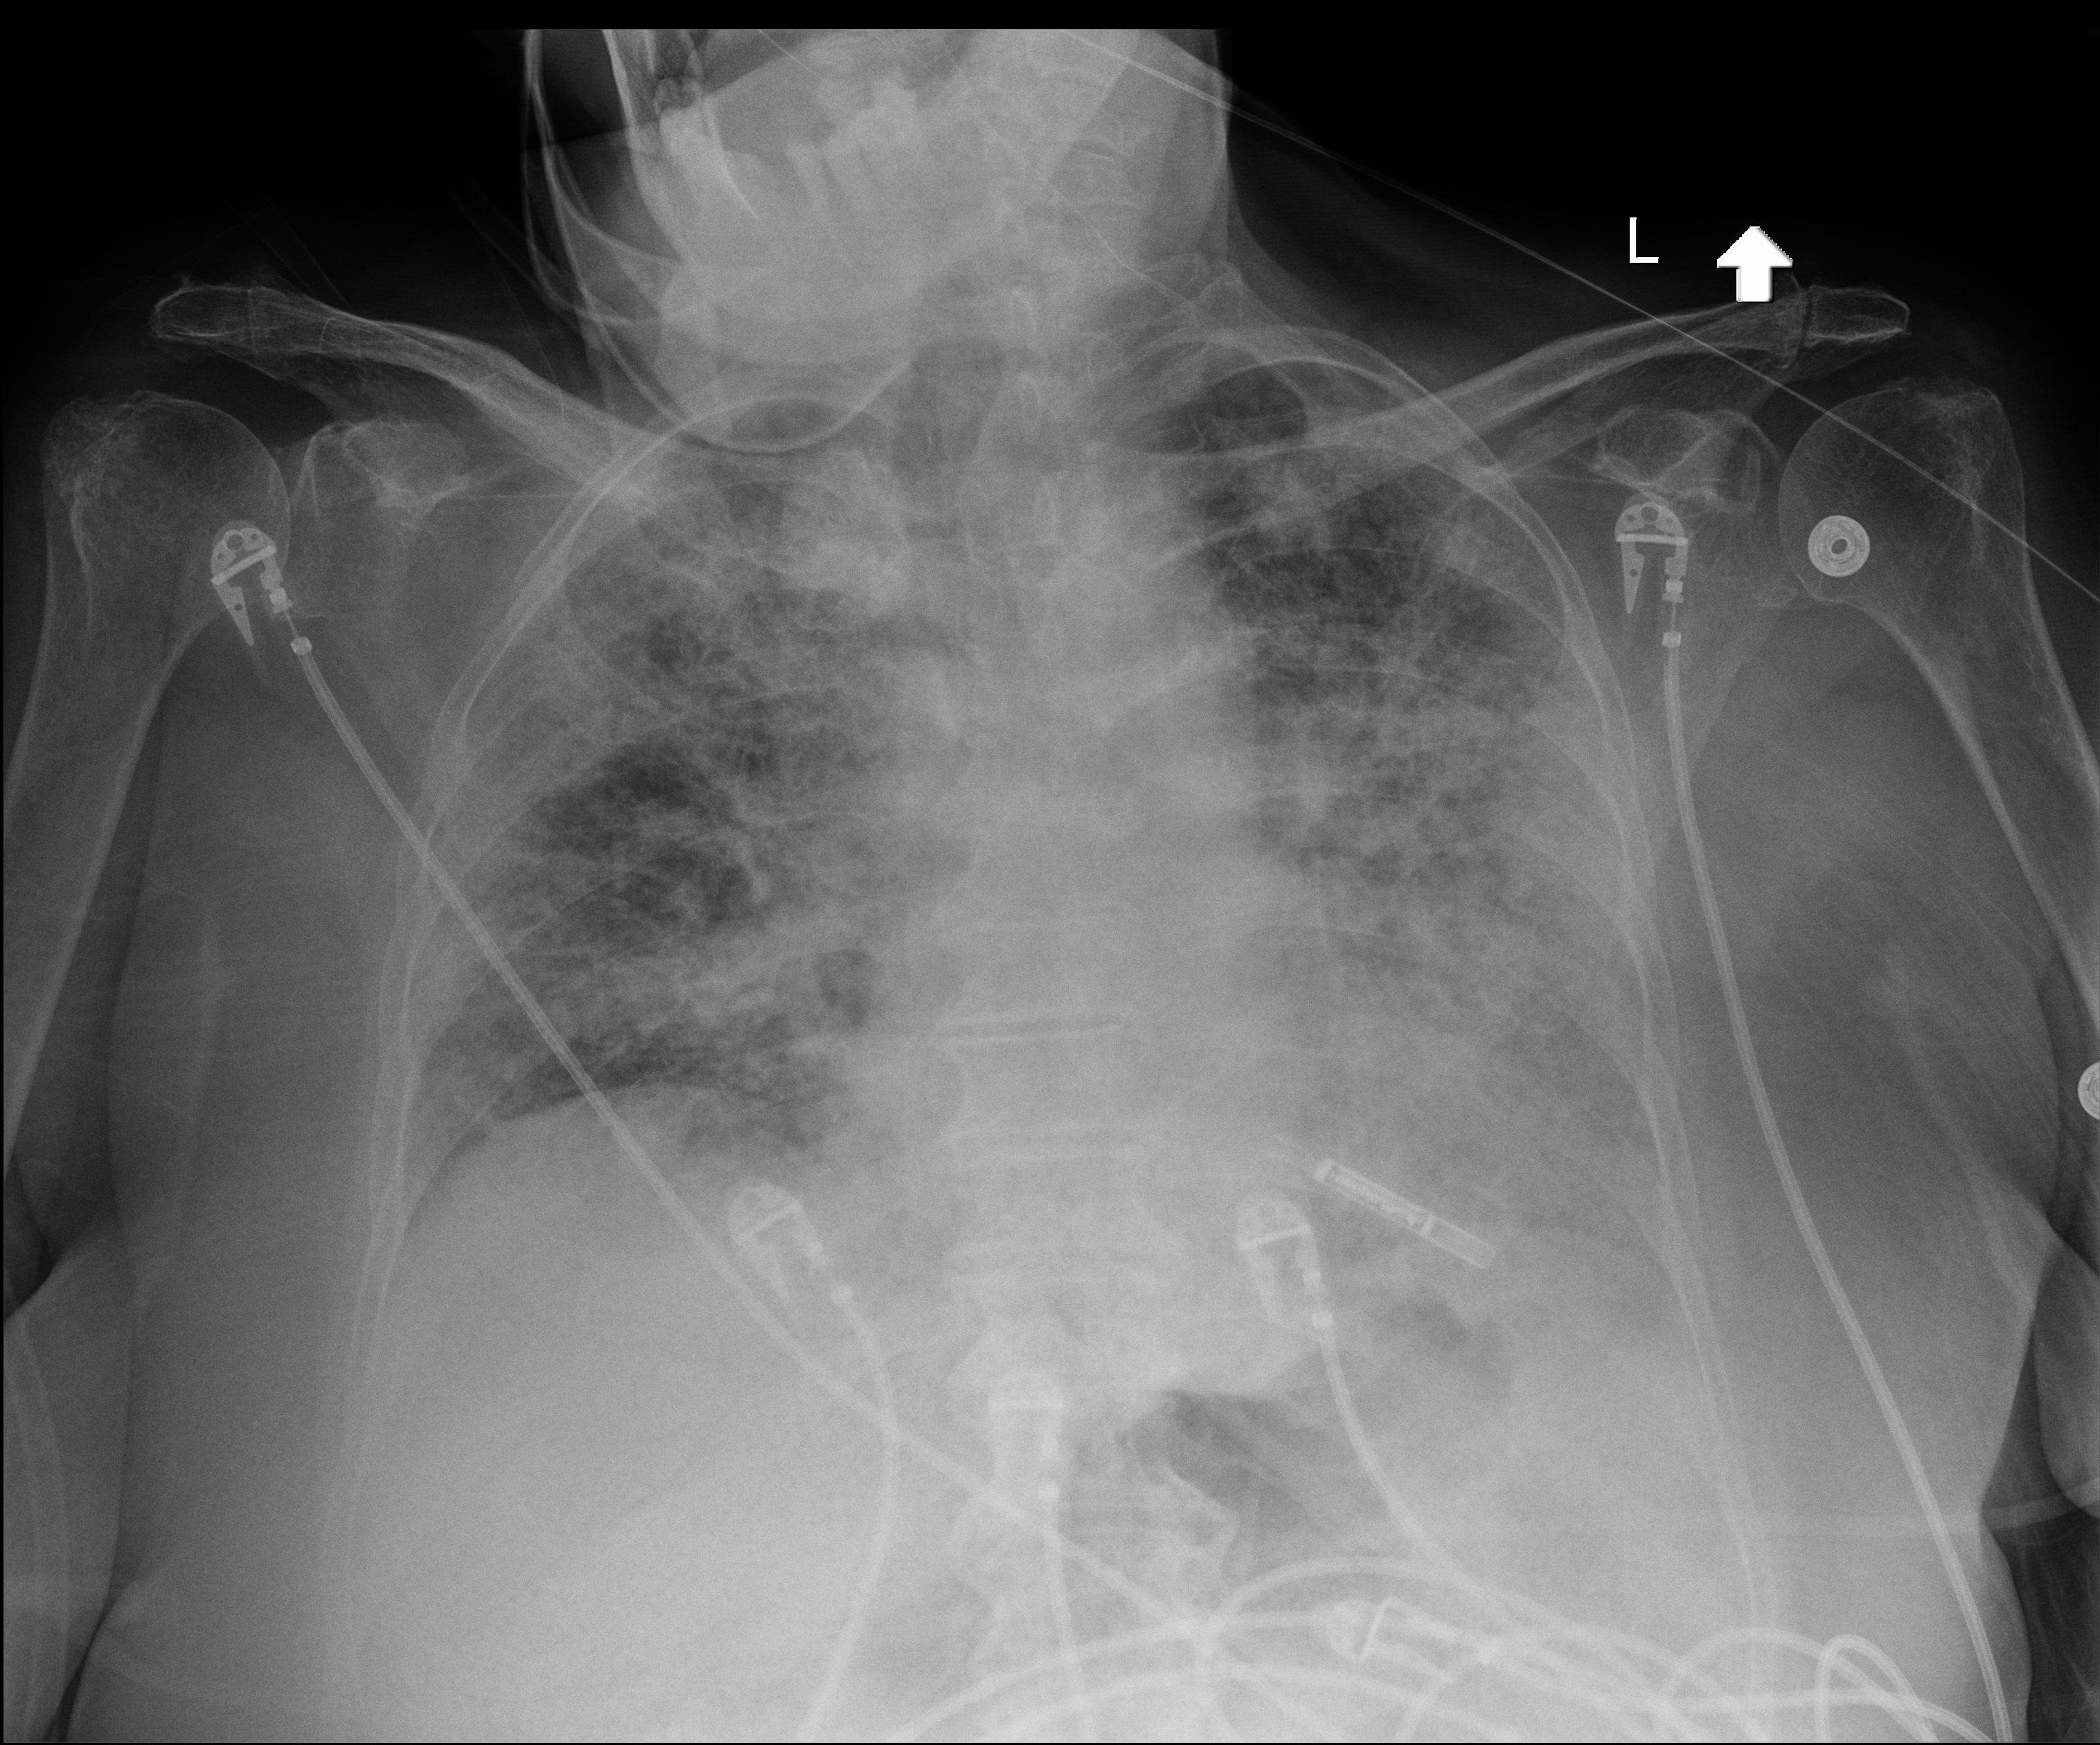
Chest radiograph (digital radiography); anteroposterior (AP) projection. Female patient hospitalised with COVID-19, age 75–90 years.
Admission-level facts for this patient (not findings on this image; timing relative to this image not recorded):
- admitted to intensive care during this hospital stay: no